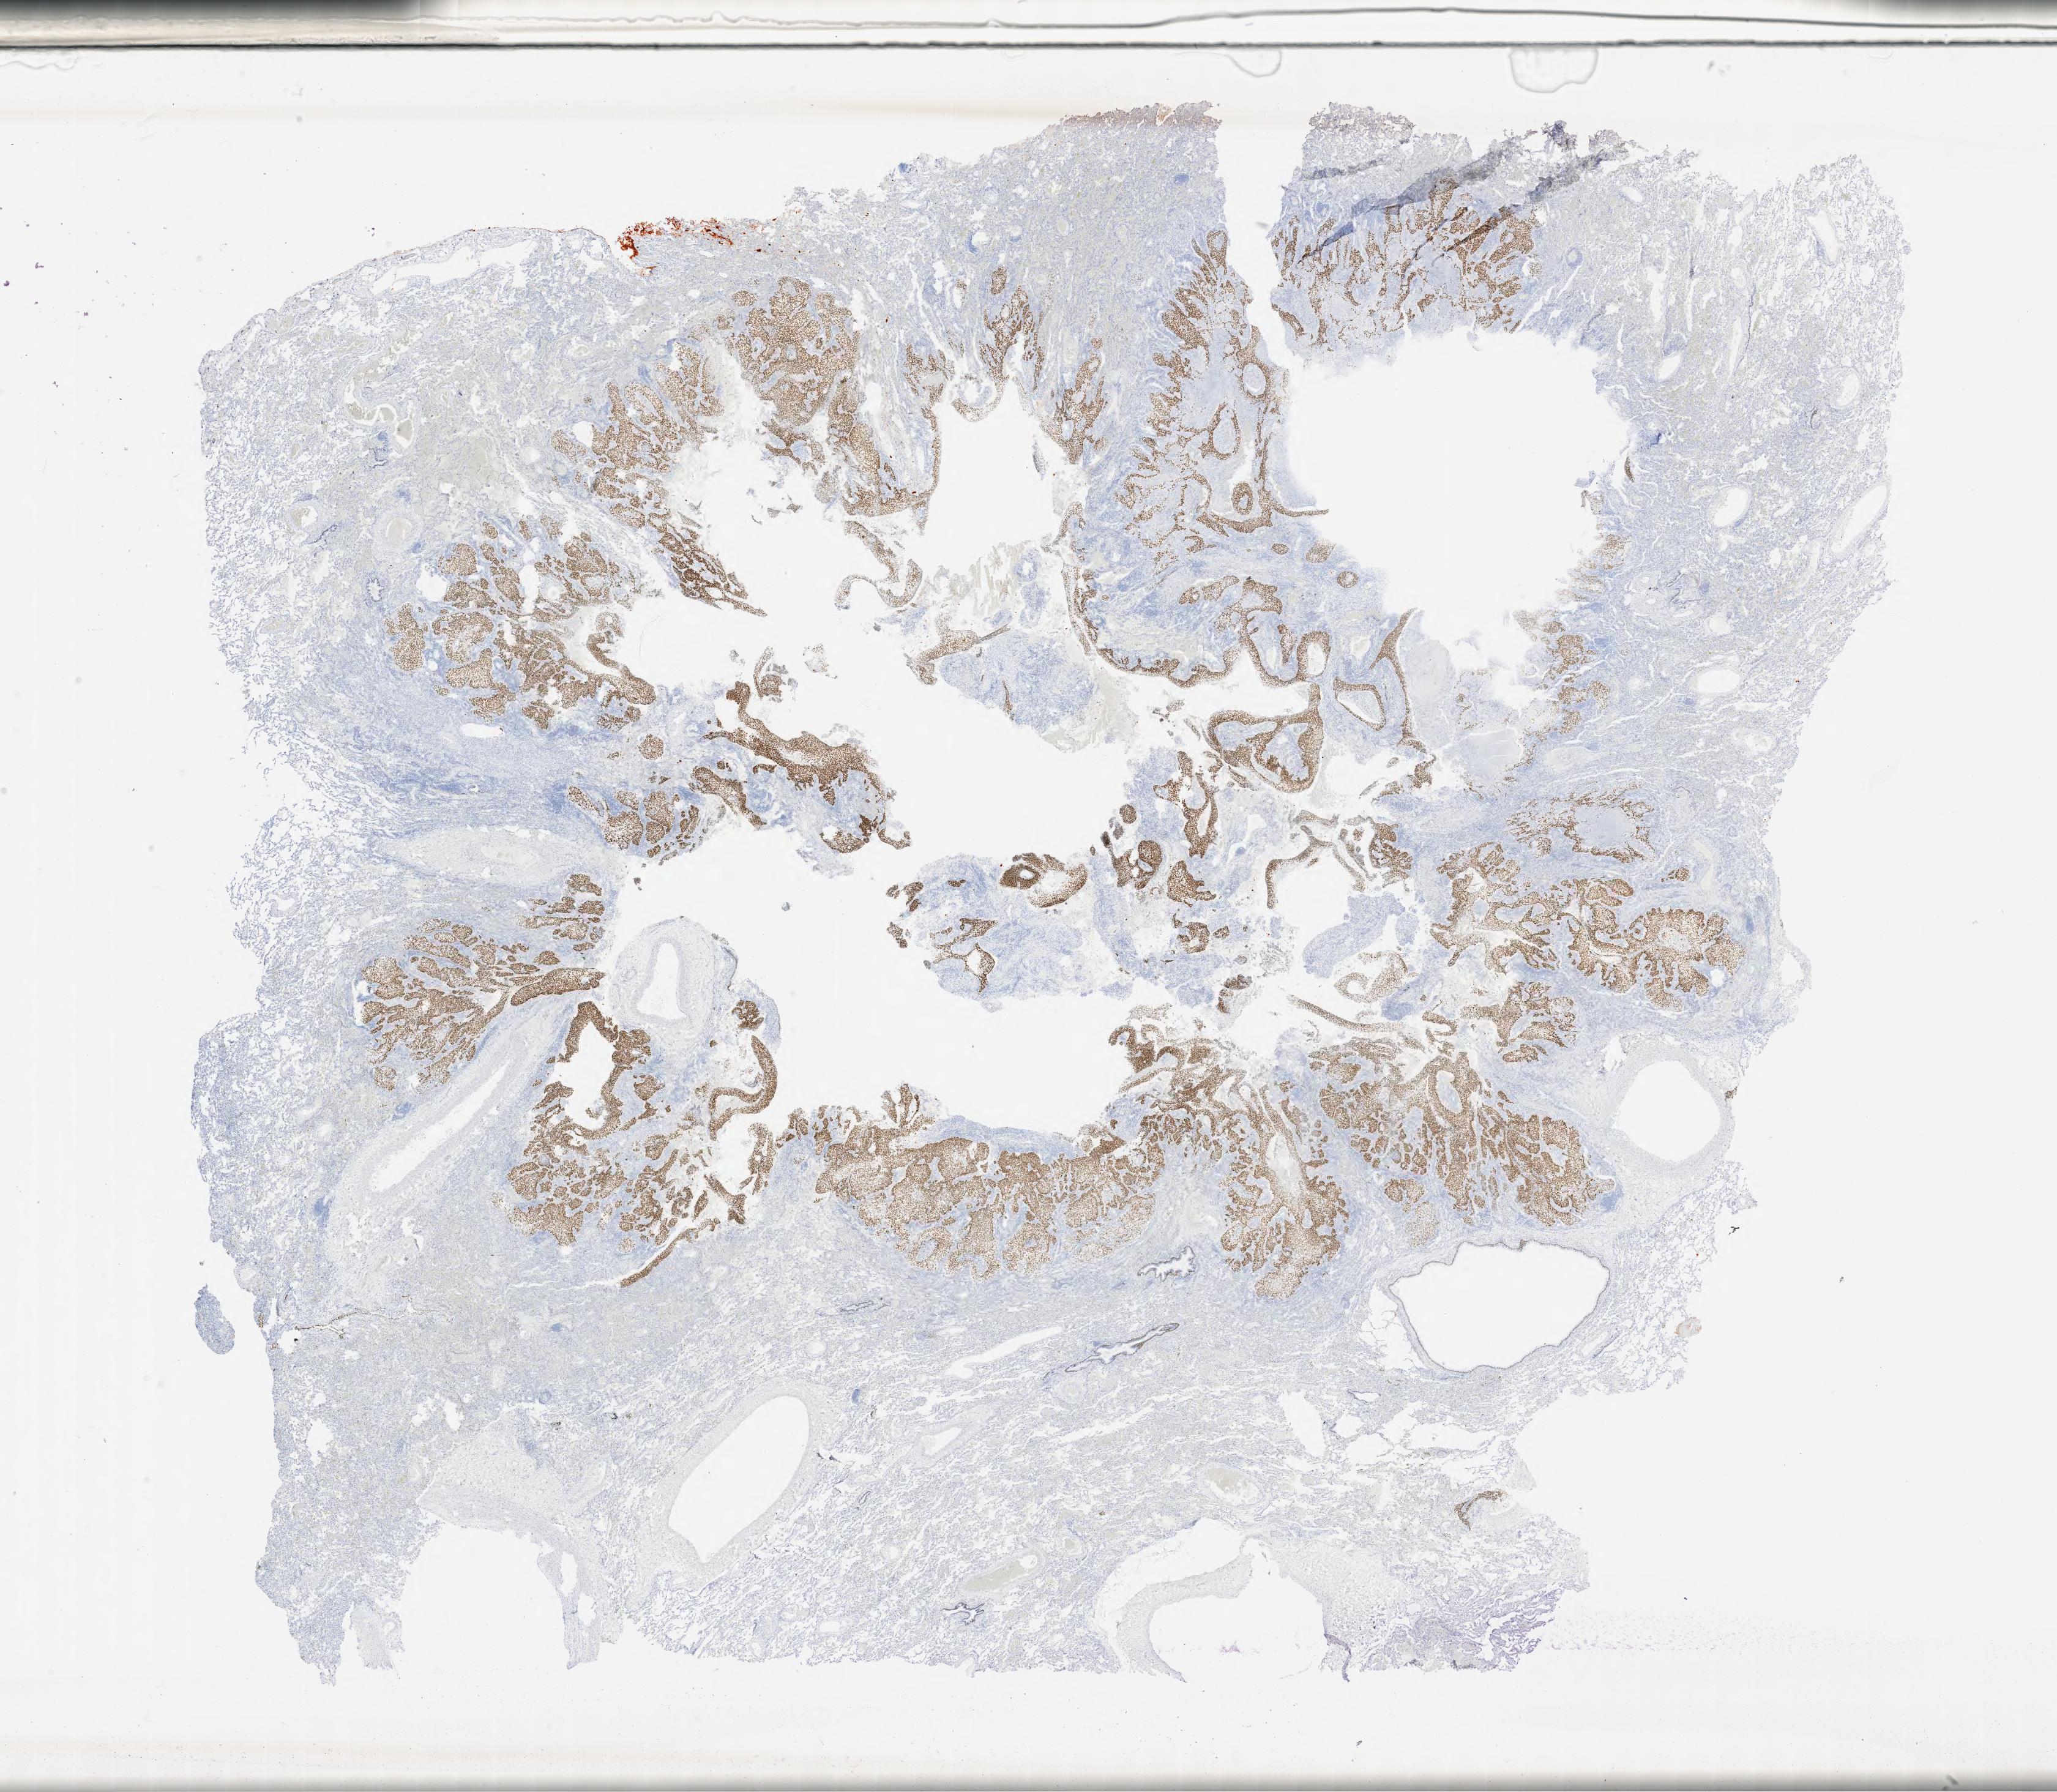
Whole-slide image, immunohistochemical stain for p40, low-resolution overview of the scanned area, about 27.2 x 23.7 mm; specimen: tumor tissue; anatomic site: lung. Male patient.
Histologic diagnosis: Squamous cell carcinoma, NOS.